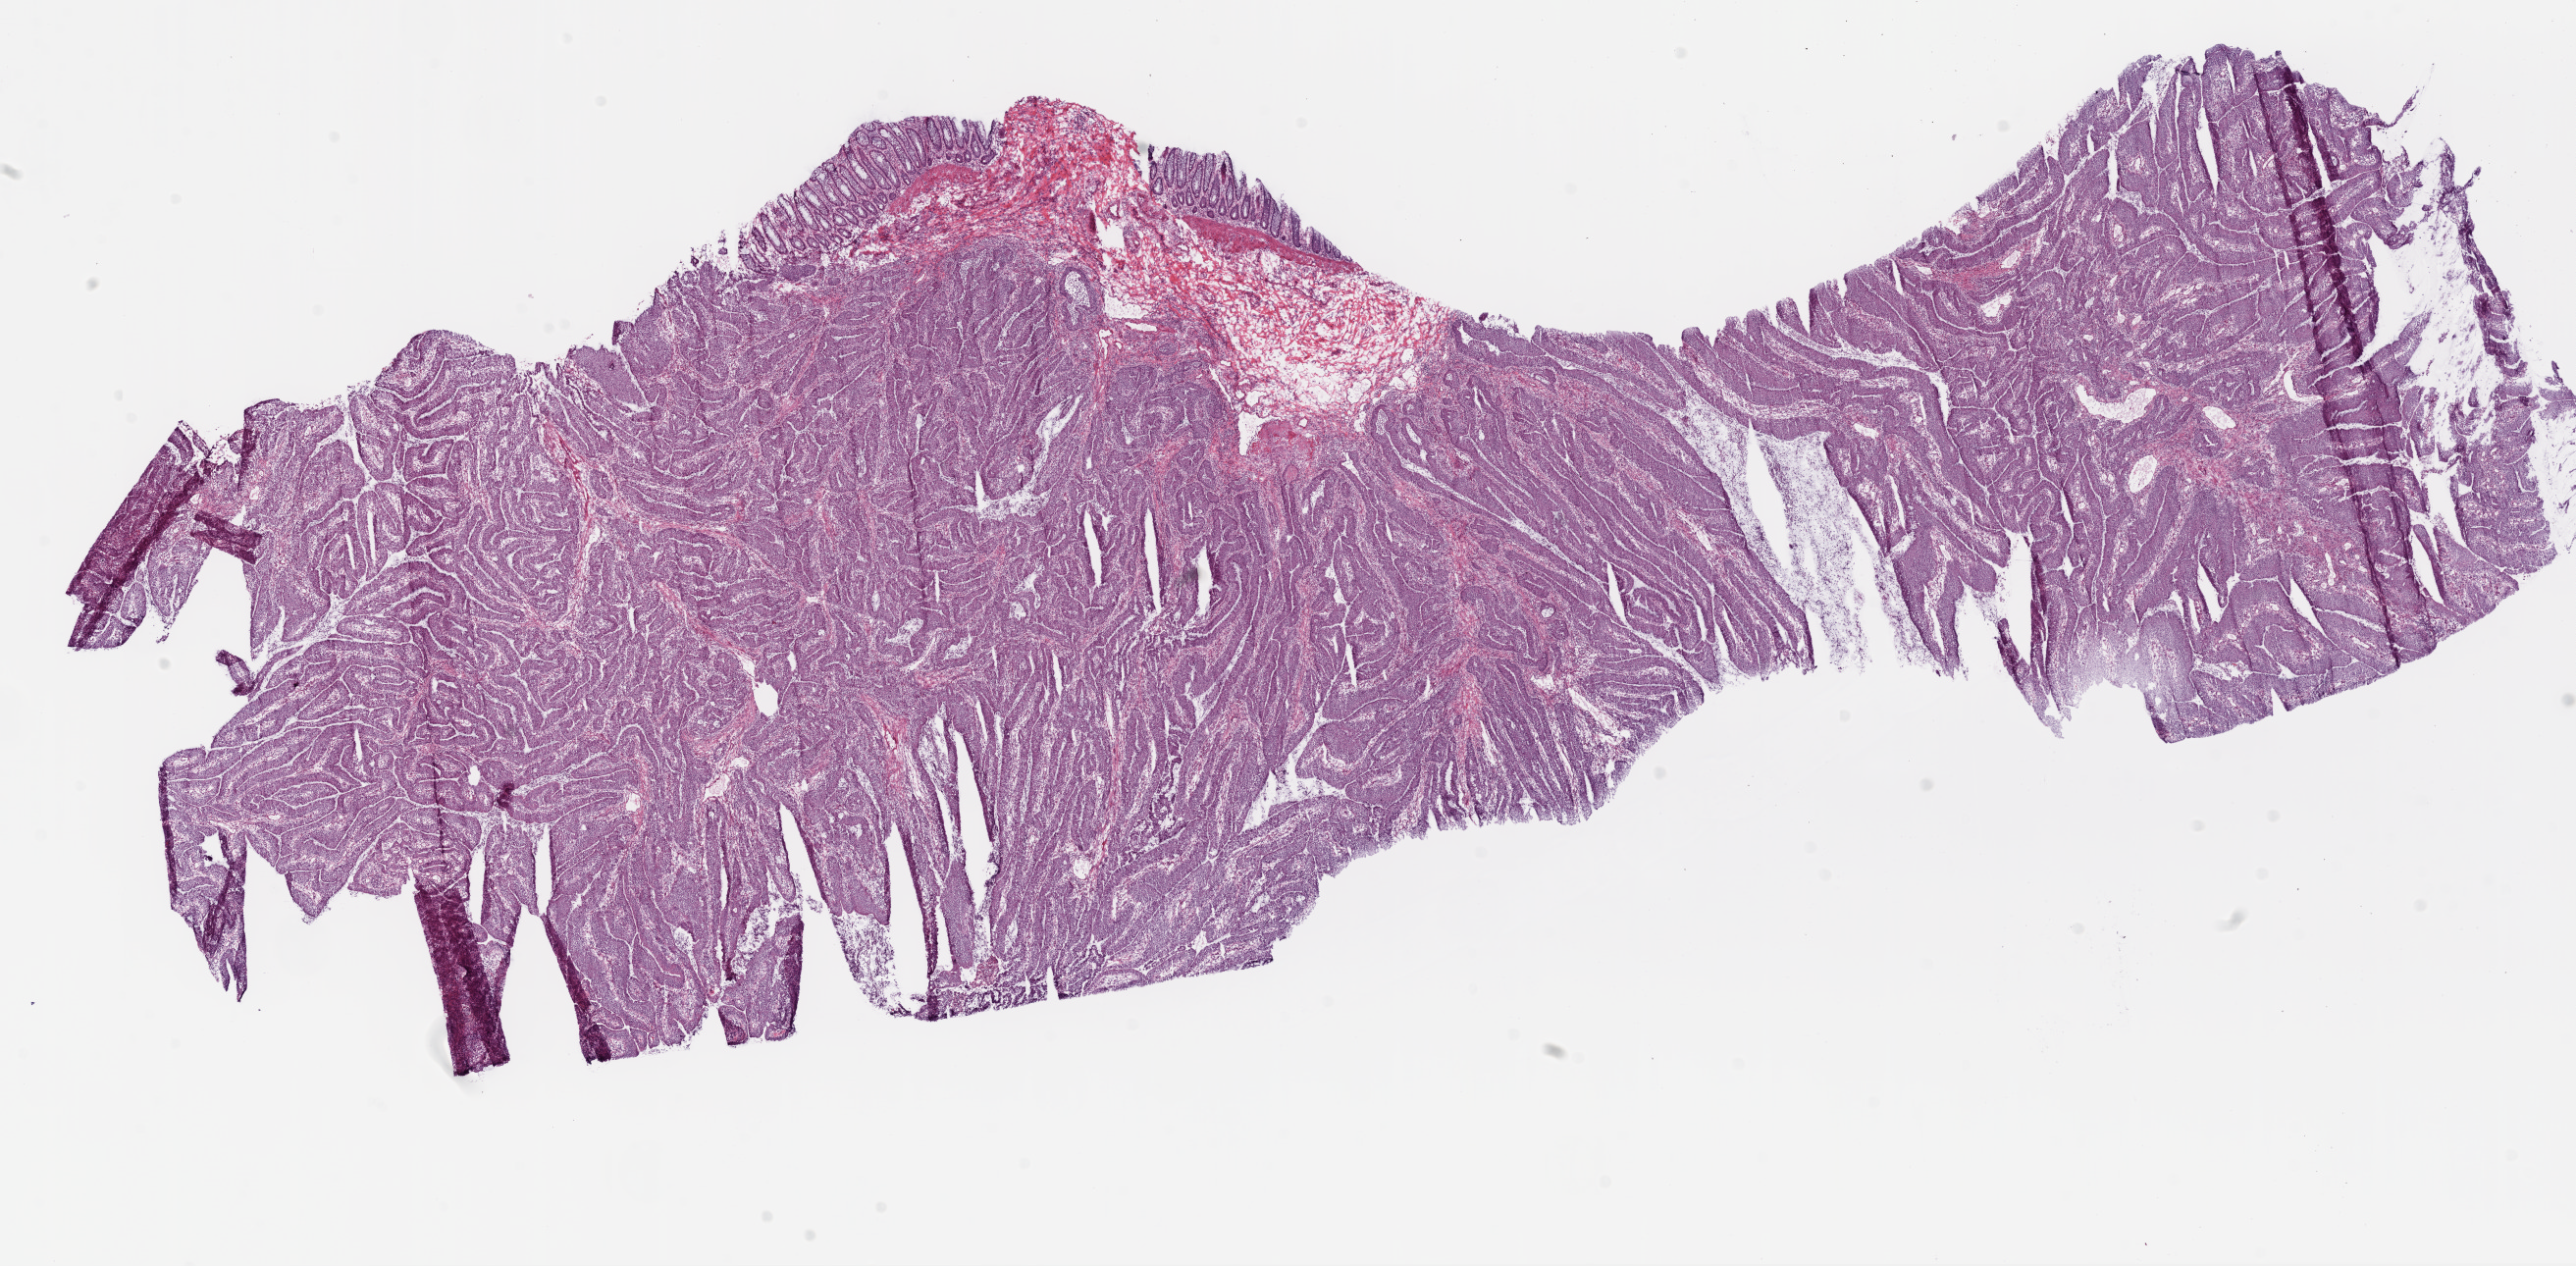
Hematoxylin and eosin (H&E) stained whole-slide image, shown as a low-resolution overview of the whole scanned area (about 21.1 x 10.4 mm, slide scanned at 20x), frozen section, sample: primary tumour, rectum. Male, age 77 years at initial diagnosis. Composition of this section per pathologist review: tumour cells 87%, tumour nuclei 85%, normal cells 3%, stromal cells 10%, necrosis 0%. Inflammatory infiltration, as recorded: lymphocyte infiltration 10%.
Histologic diagnosis: Mucinous adenocarcinoma (rectosigmoid junction). TNM: T3 N0 M0. Lymph nodes positive (case pathology): 0 of 25 examined. AJCC pathologic stage: IIA (6th edition).